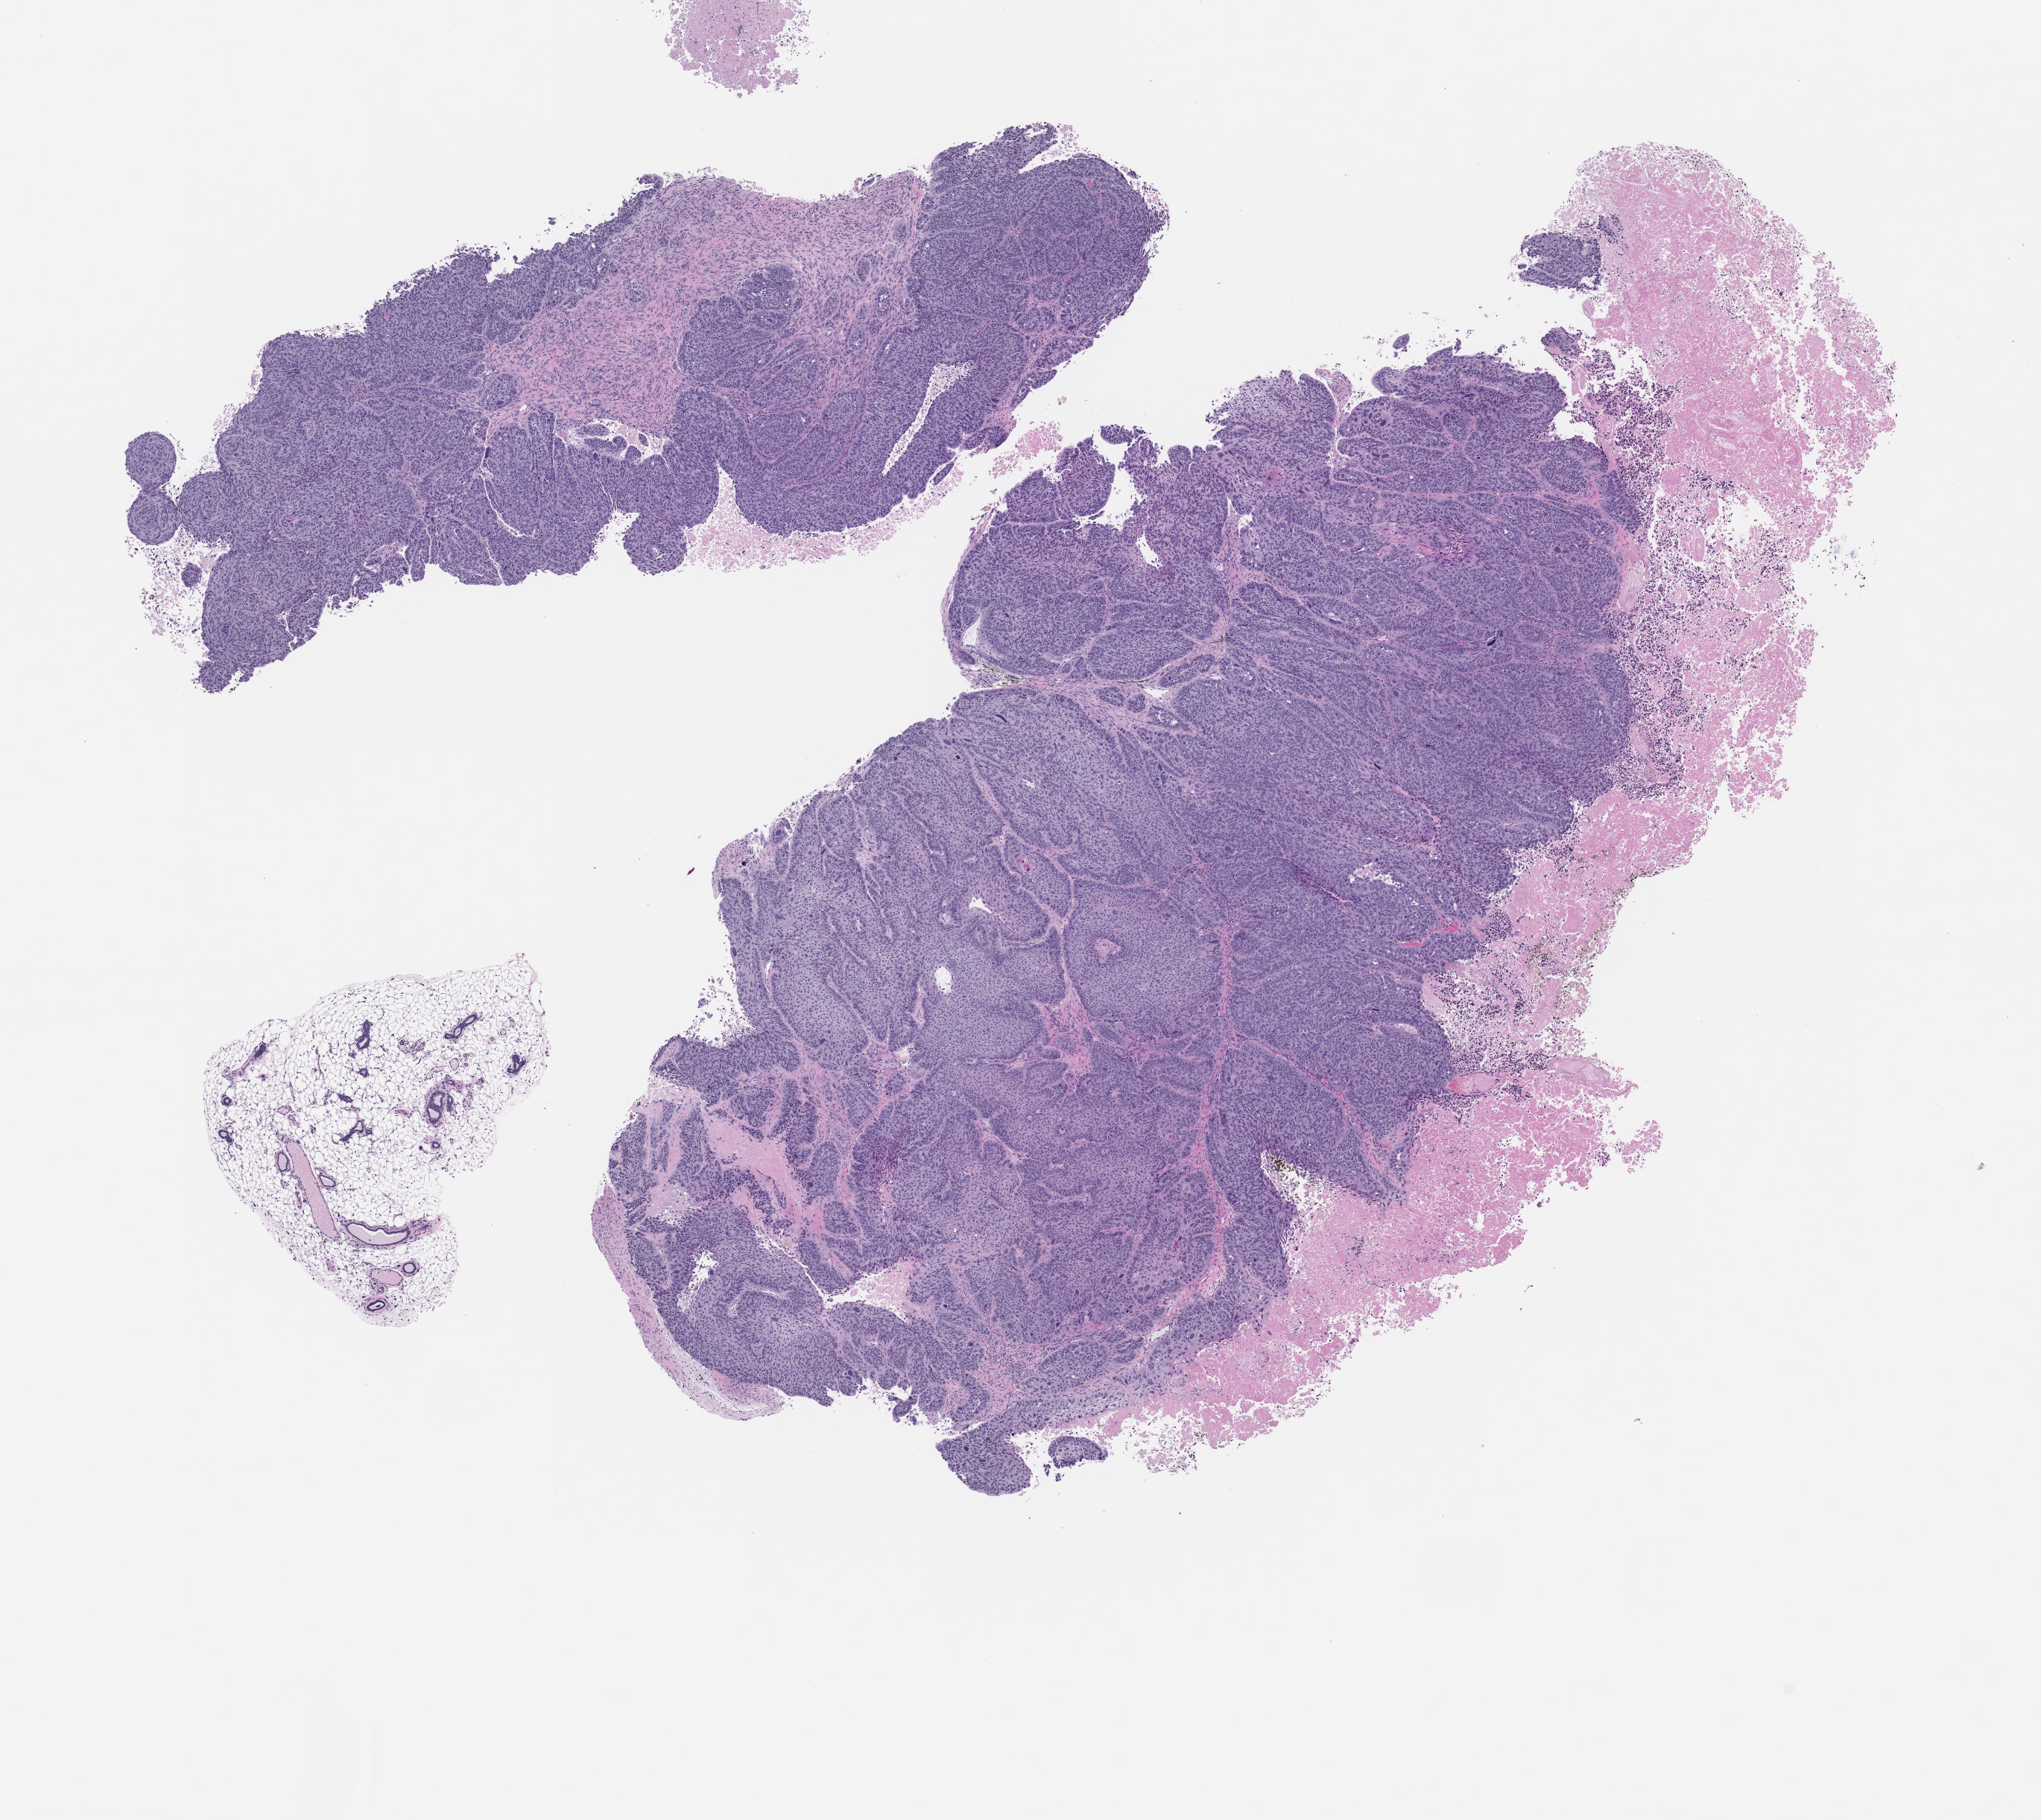
Hematoxylin and eosin (H&E) whole-slide image of a patient-derived xenograft (PDX) tumor grown in a mouse — a low-resolution overview of the entire scanned area, about 11.0 x 9.8 mm; FFPE section; originating tumor site category: lung.
Originating patient diagnosis: Lung Squamous Cell Carcinoma.